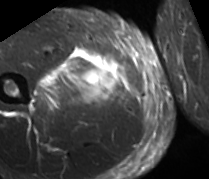
MRI of an extremity soft-tissue mass, one axial slice. Slice 29 of 89 in the series (ordered by position). STIR. MR volume resampled by the dataset authors to the PET/CT grid (not the native acquisition matrix). 3.27 mm slice thickness. 209 × 179 image matrix, field of view 204 × 175 mm. Male patient. Case-level facts recorded for this patient, not image findings: histological type: undifferentiated - pleiomorphic; grade: high; site of the primary tumour: right thigh.
Annotated regions visible in this slice (expert contour drawn on MRI and transferred to this co-registered scan by the dataset authors):
- gross tumour volume including surrounding oedema: bounding box <30,46,115,108> (left, top, right, bottom; pixels)
- gross tumour volume (mass): <76,62,115,95>